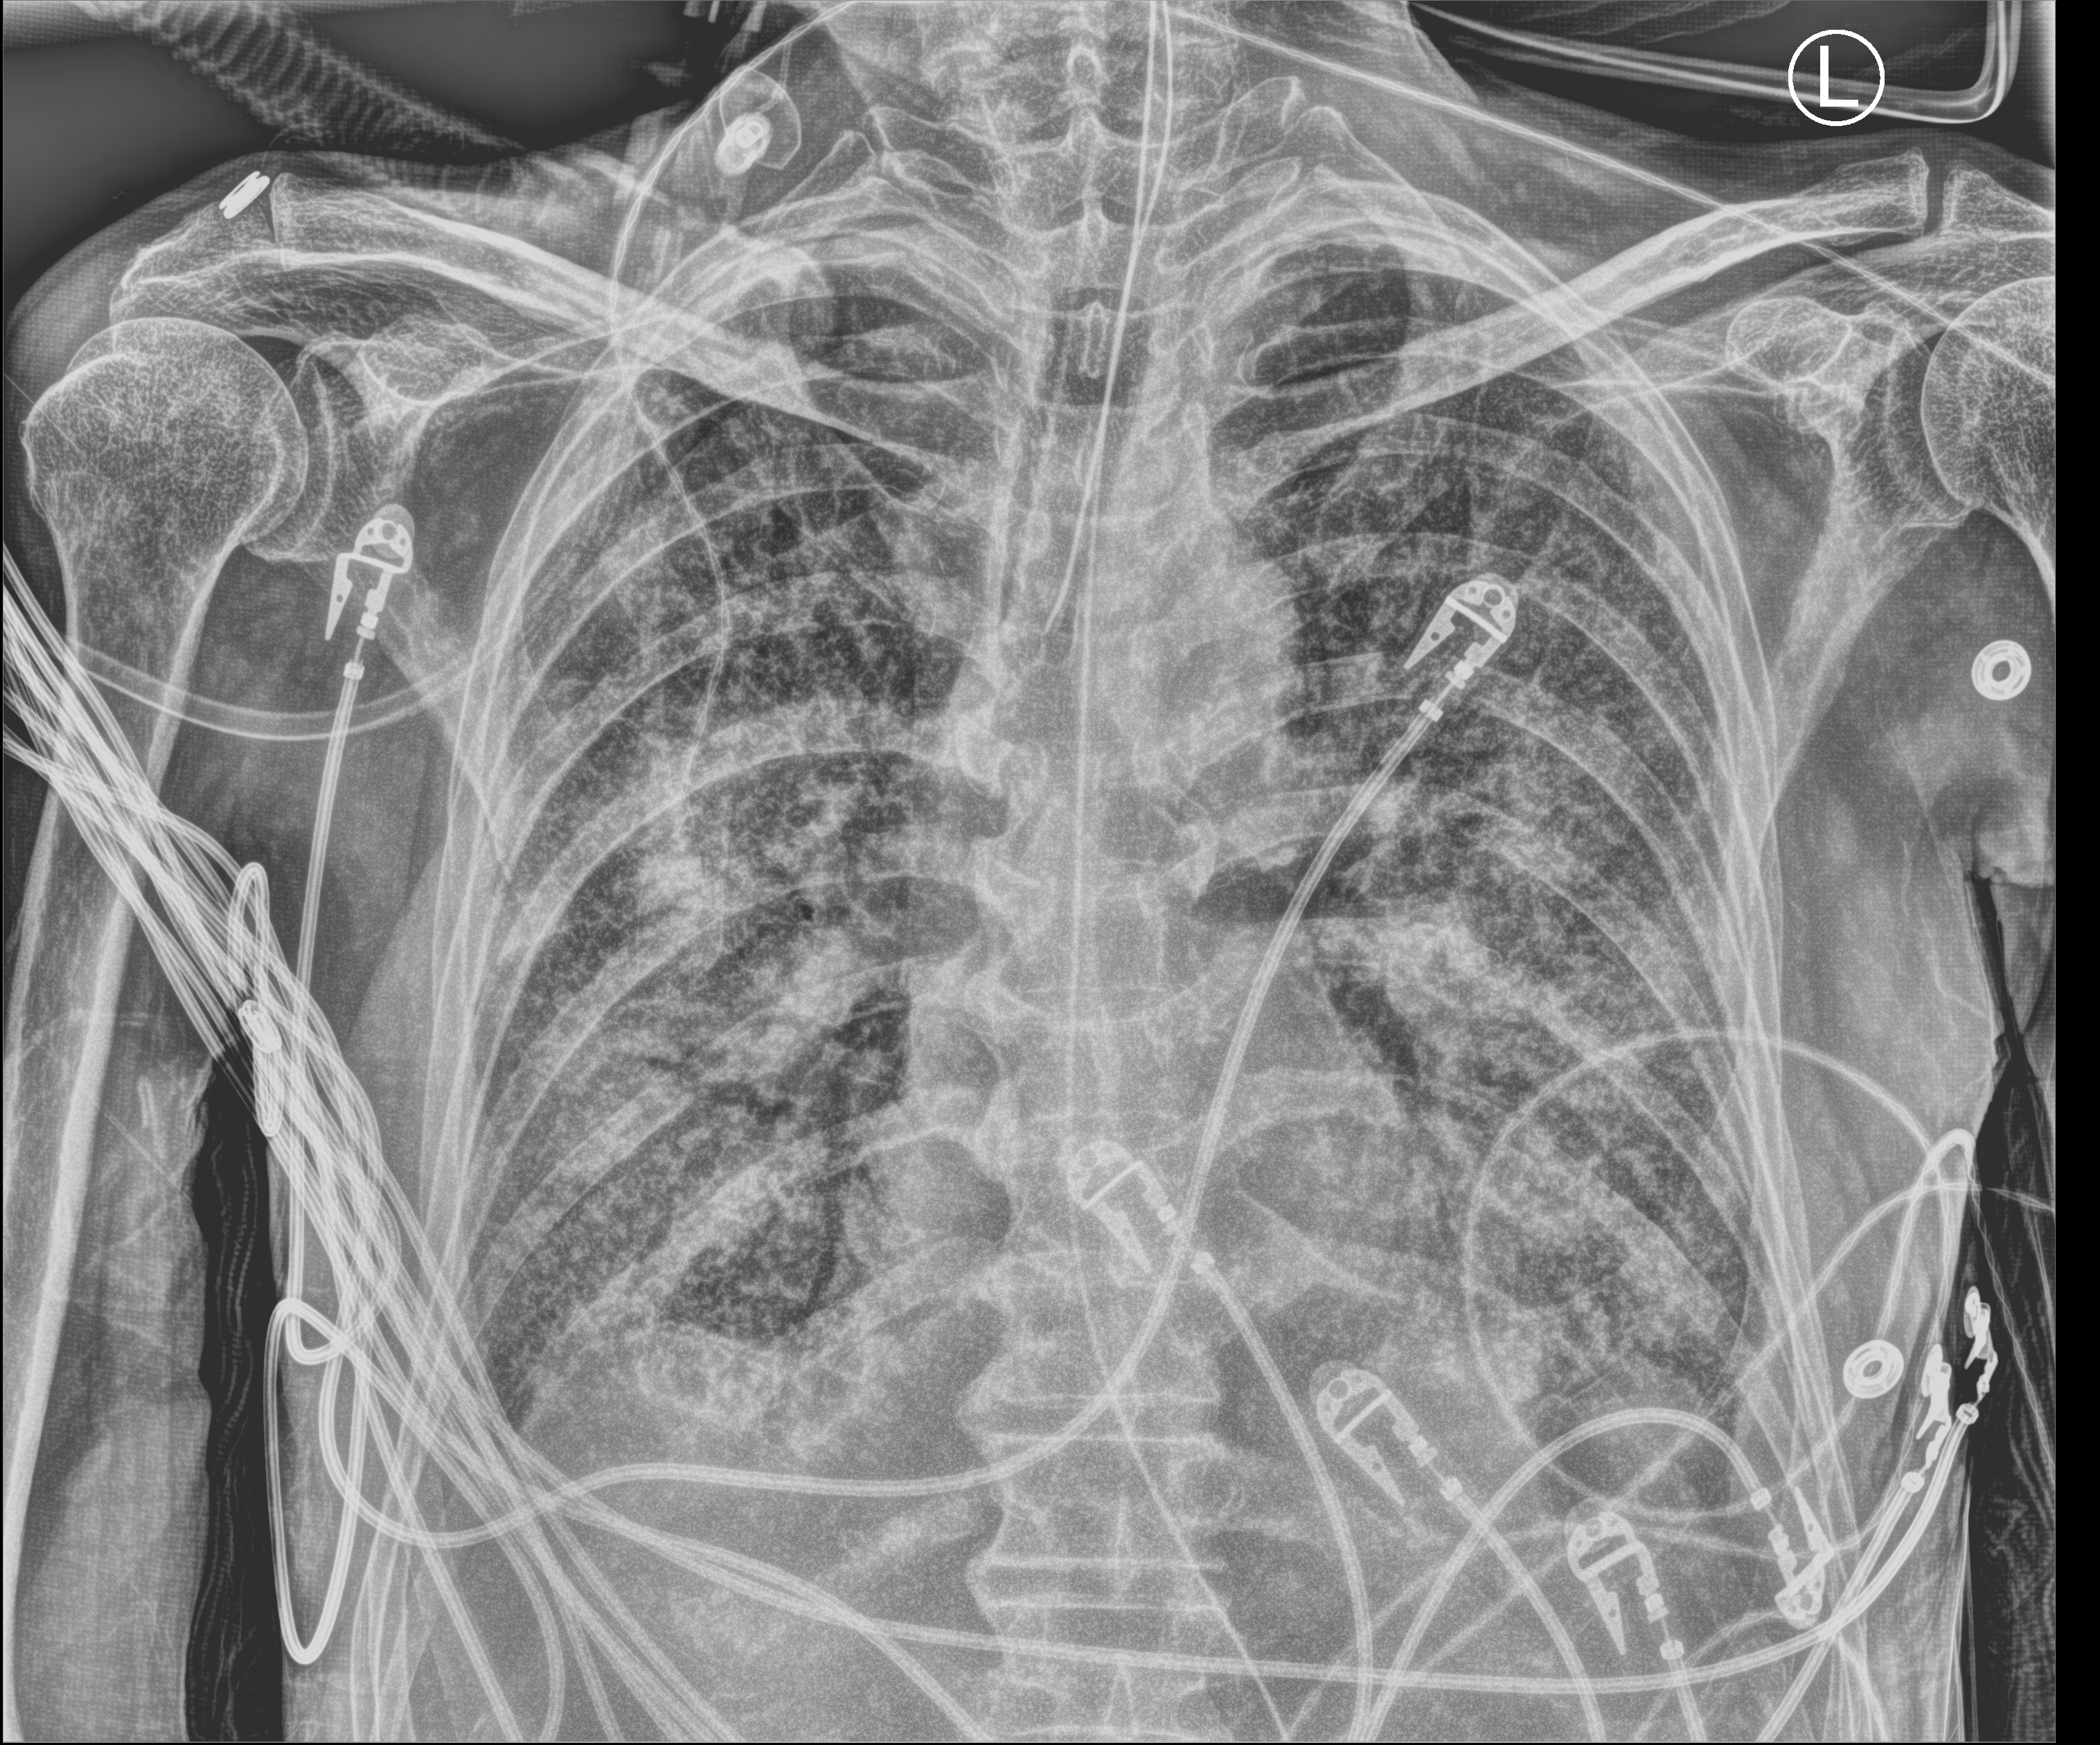
Portable chest radiograph; anteroposterior (AP) projection. Male patient hospitalised with COVID-19, age 60–74 years.
From the hospital-stay record, not from the radiograph (when in the stay this image was taken is not recorded):
- diabetes (admission record): yes